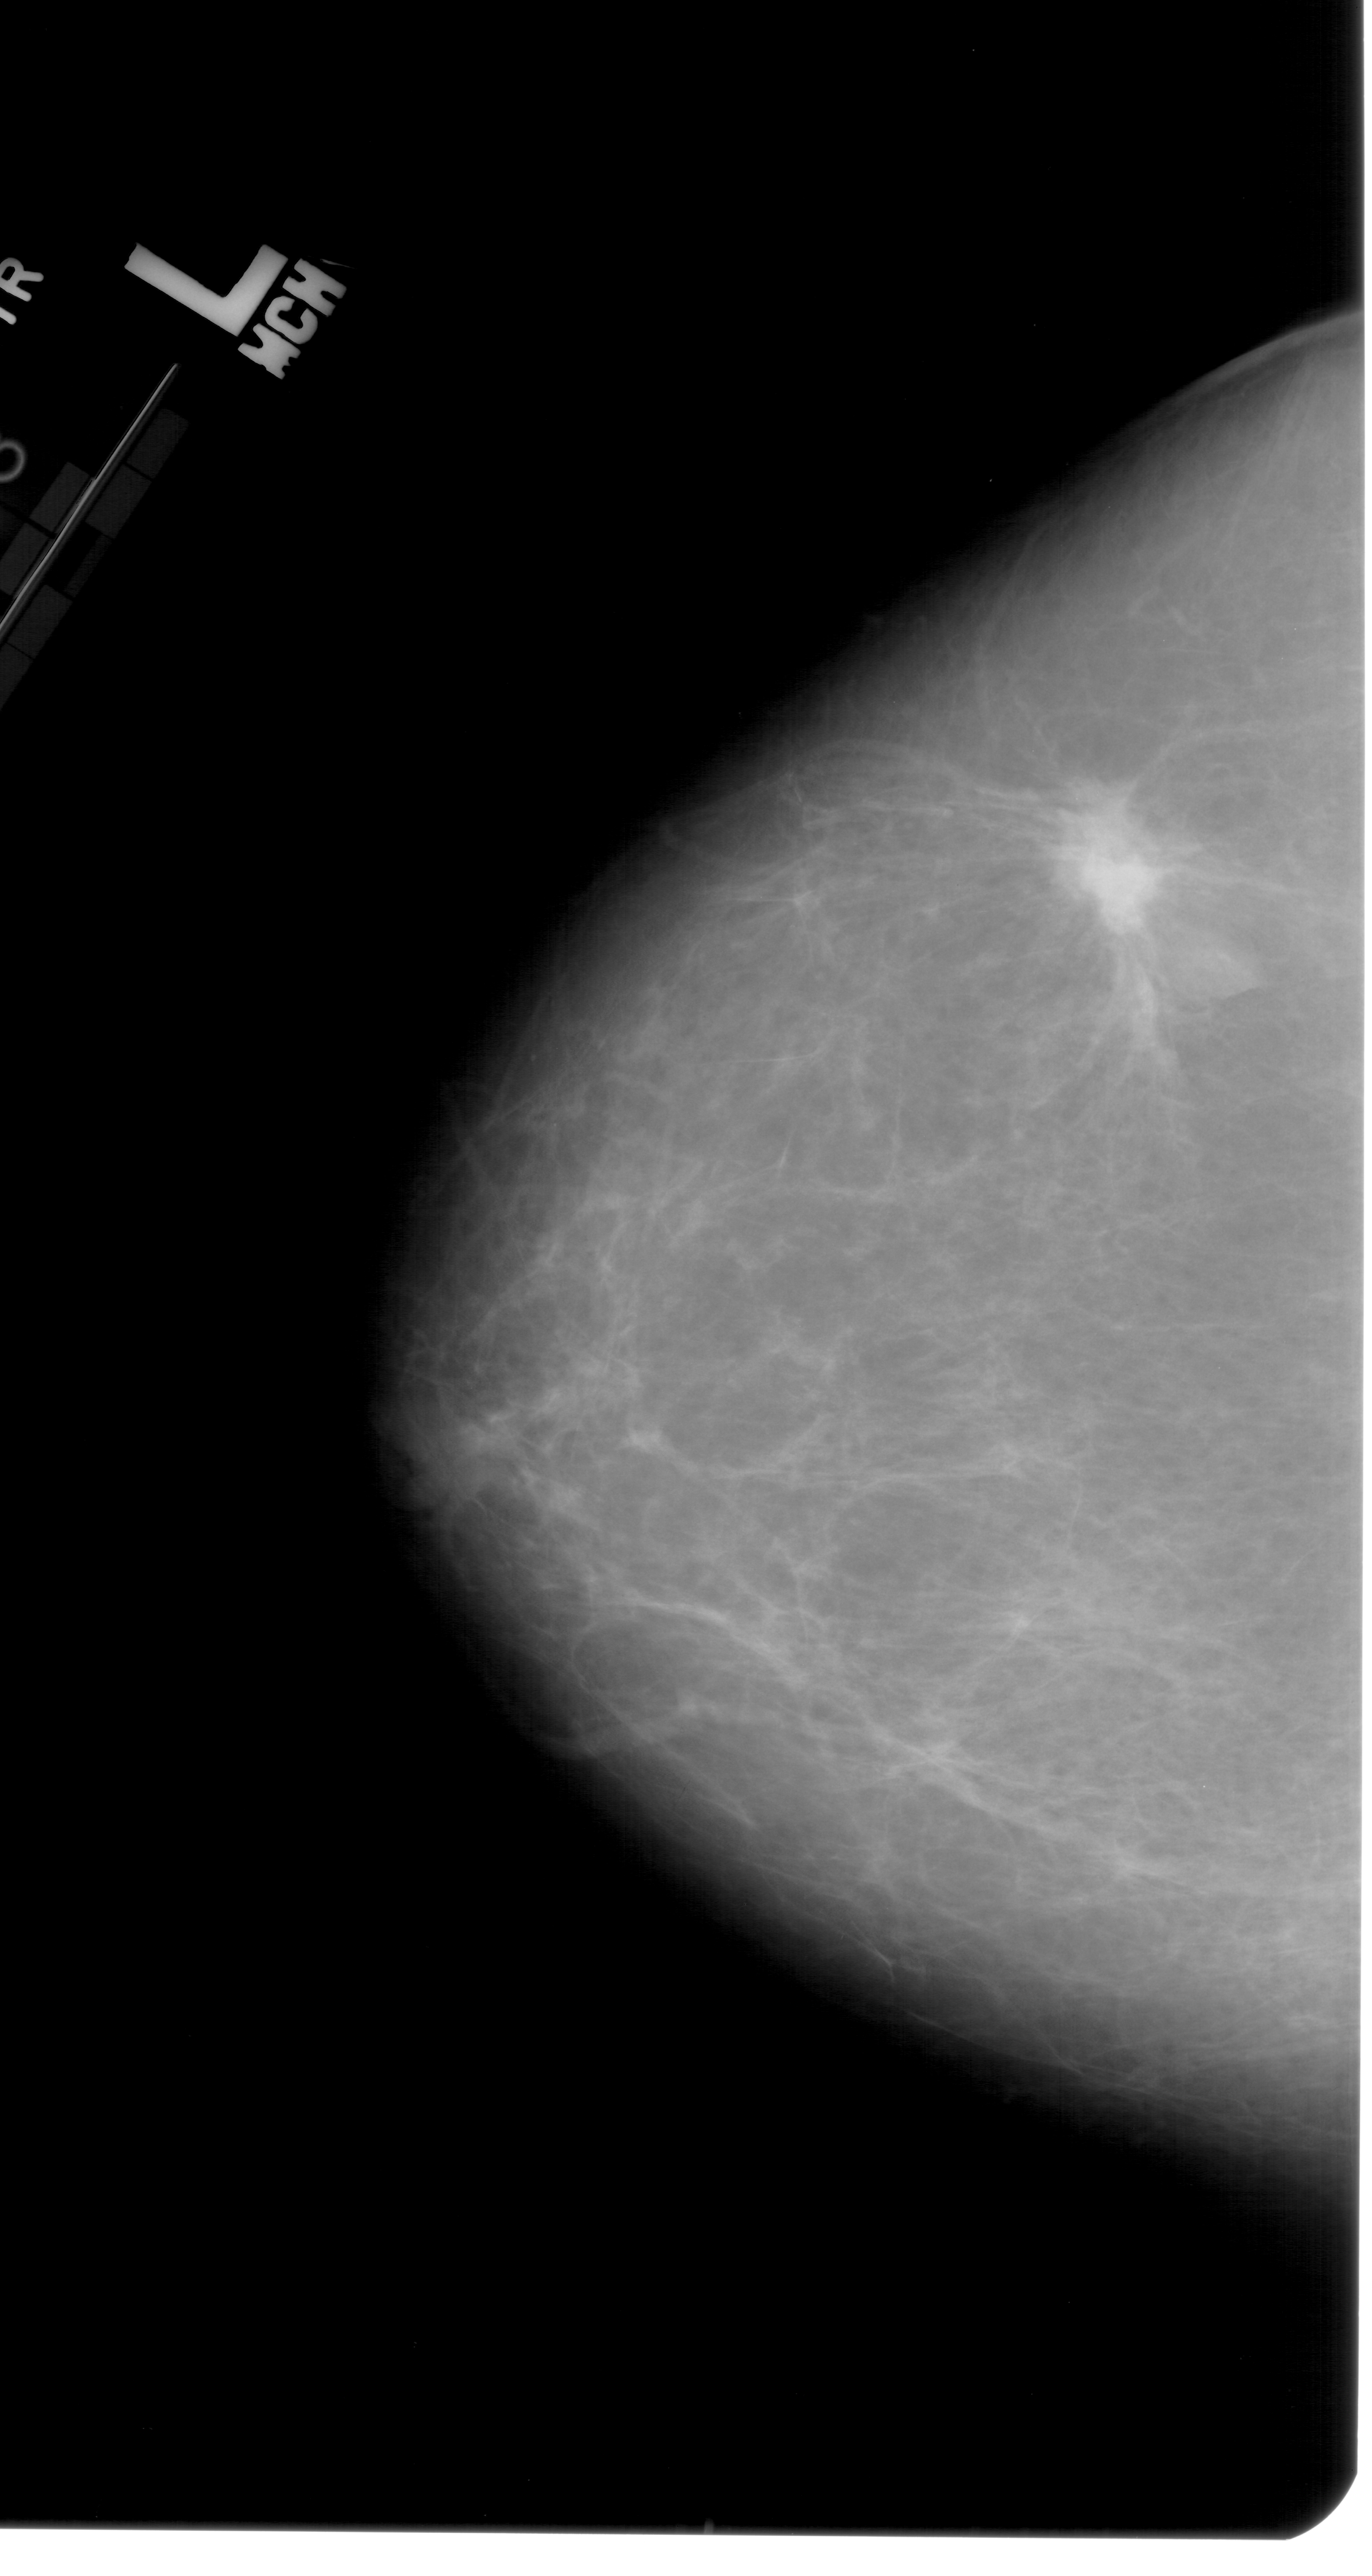
Mammogram (digitized film); left breast; CC view; BI-RADS breast density category 2 (scale 1–4); 1372 × 2576 image matrix.
Expert-marked regions of interest on this image (one box per marked abnormality):
- mass, shape irregular, margins spiculated; BI-RADS assessment category 5; subtlety rating 5 on a 1 (subtle) to 5 (obvious) scale; pathology (as recorded): malignant: box from (x=1022, y=812) to (x=1191, y=971) px